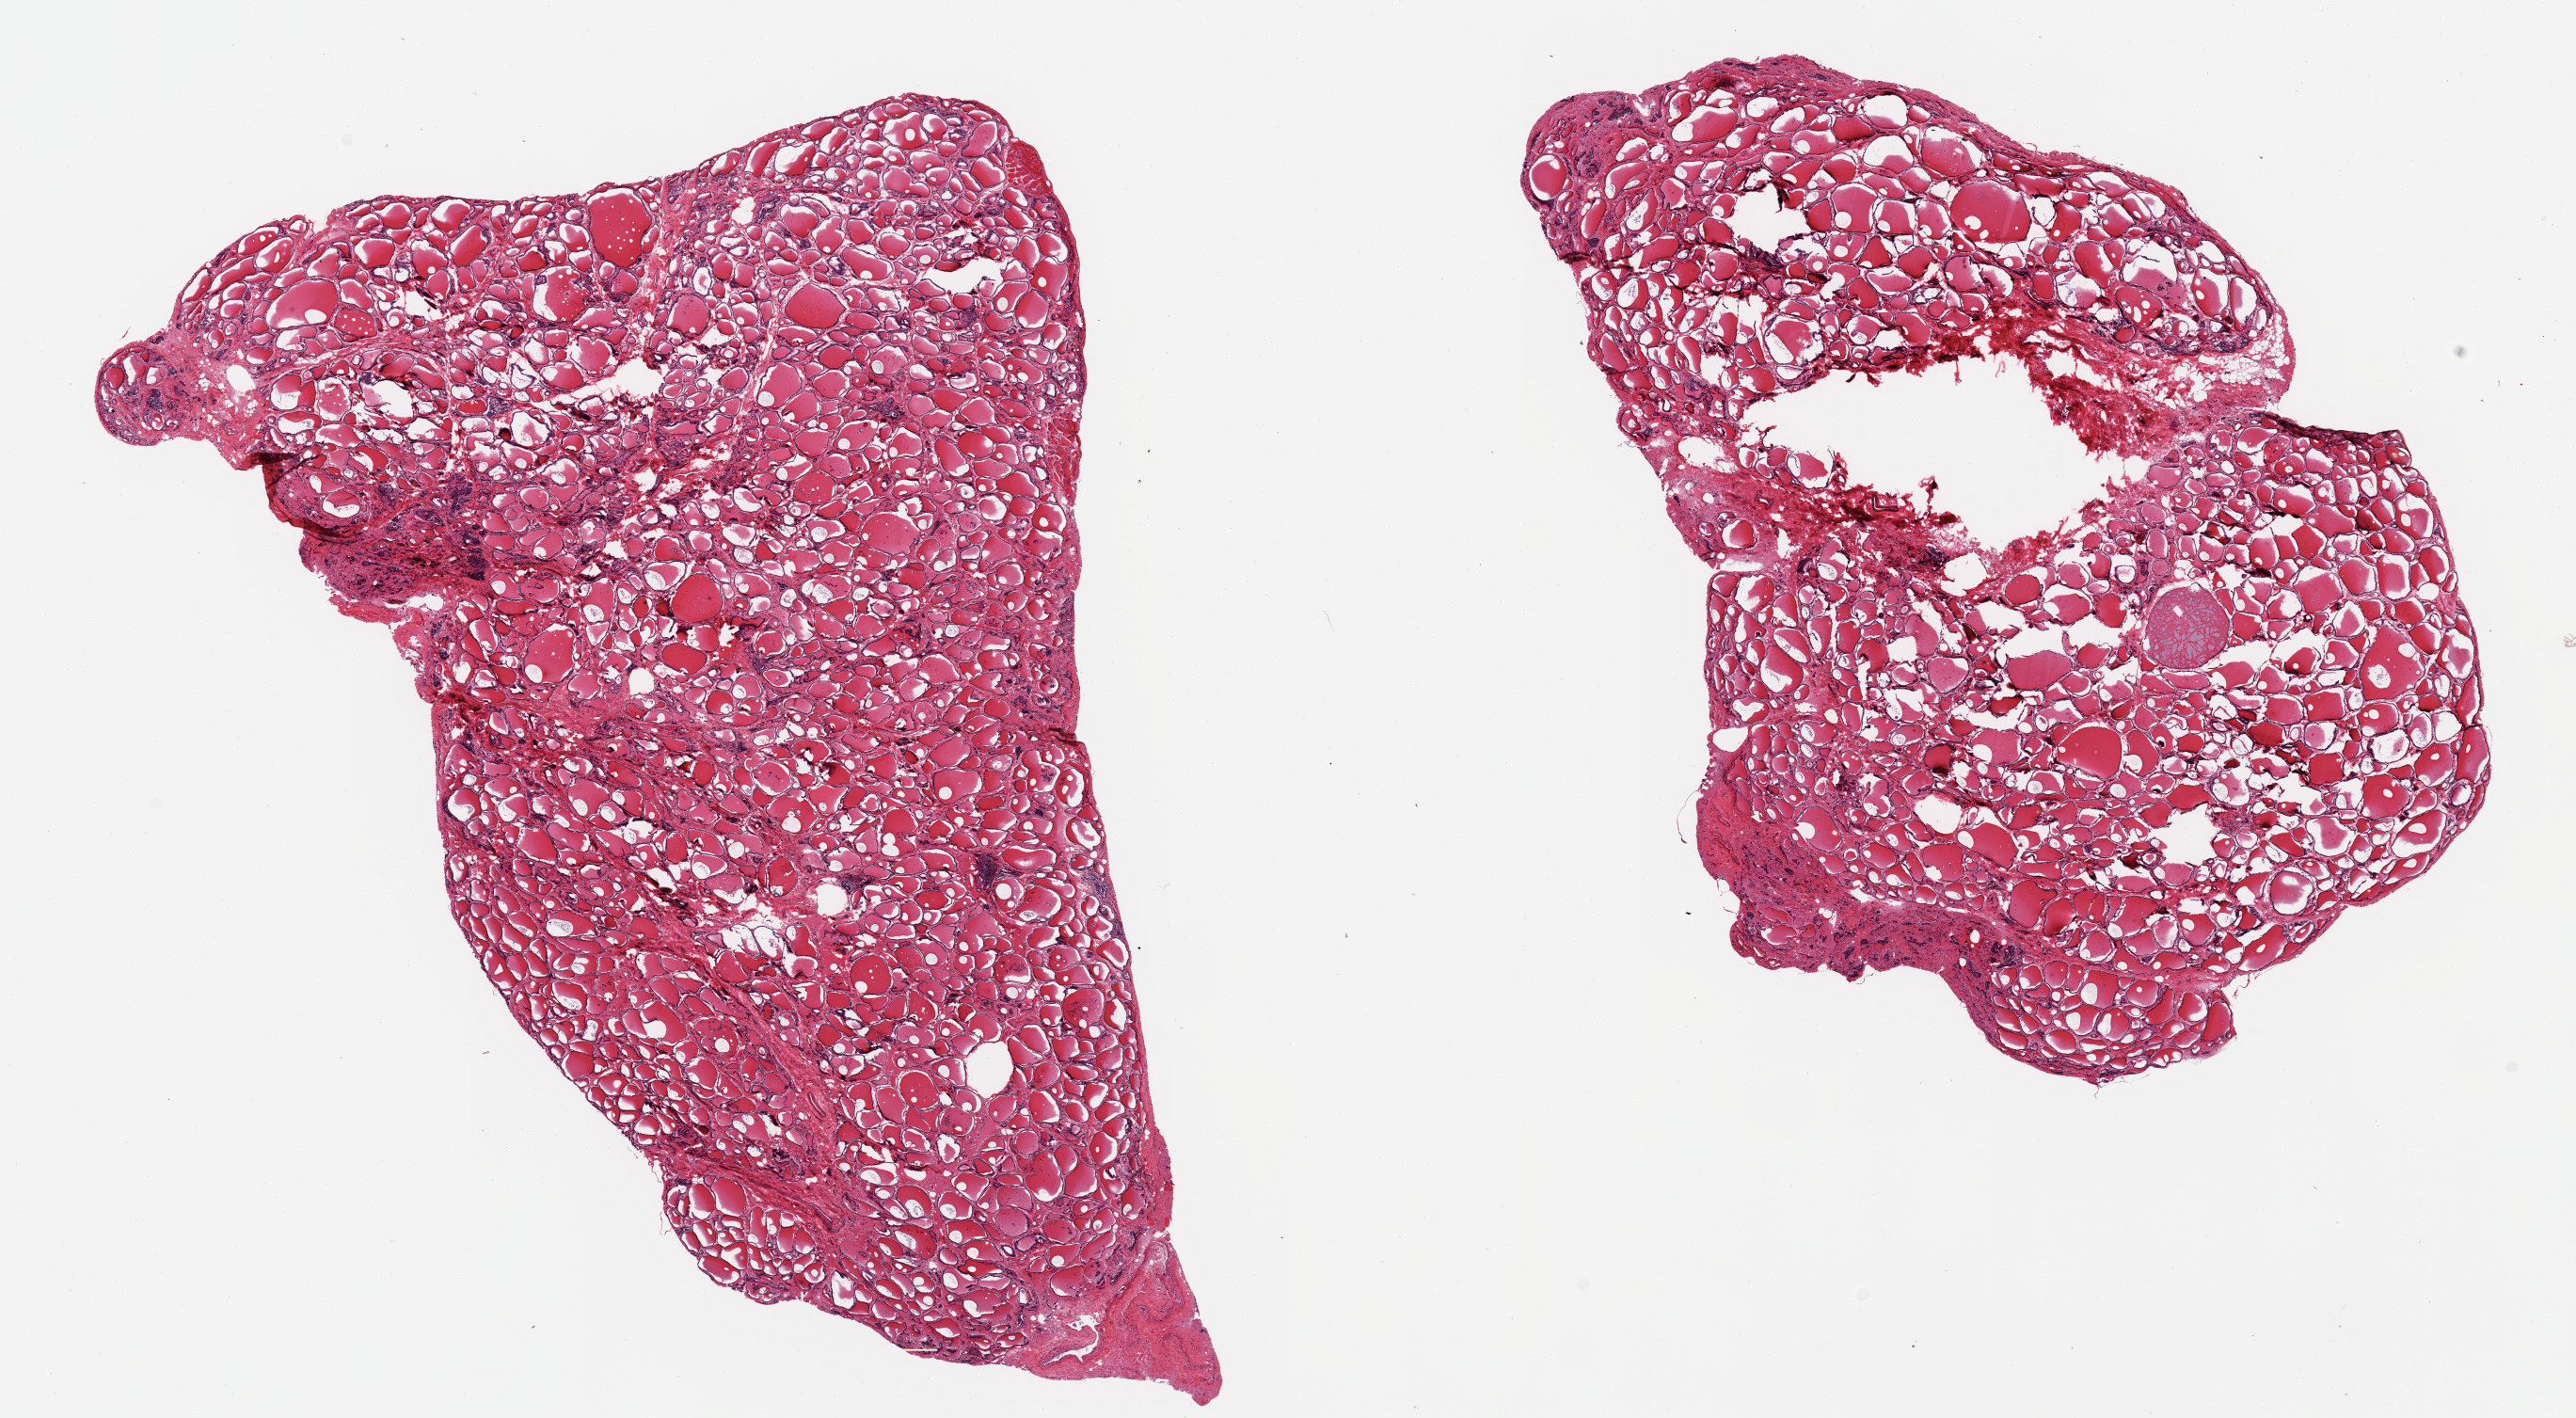
Digitized hematoxylin and eosin (H&E)-stained section — shown as a low-resolution overview of the whole scanned area (about 21.7 x 11.9 mm); PAXgene-fixed, paraffin-embedded tissue; target tissue: thyroid; donor tissue sample. Male donor.
• review note (as recorded): 2 pieces; 0.7 mm focus of crystalline material. probably colloid